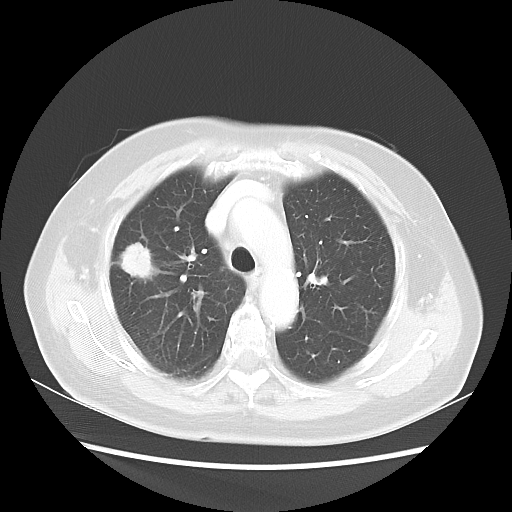
Chest CT, one axial slice; slice 34 of 48 in the series (ordered by position); 100 kVp; lung window (W 1500 / L -600 HU); 5 mm slice thickness; 512 × 512 image matrix, field of view 360 × 360 mm. Female patient, age 75 years. From the clinical record (not read from this slice): clinical TNM (as recorded): T1c N0 M0.
Annotated regions visible in this slice (bounding box drawn by a radiologist):
- lung tumour (recorded histology: adenocarcinoma): bounding box <117,238,158,284> (left, top, right, bottom; pixels)